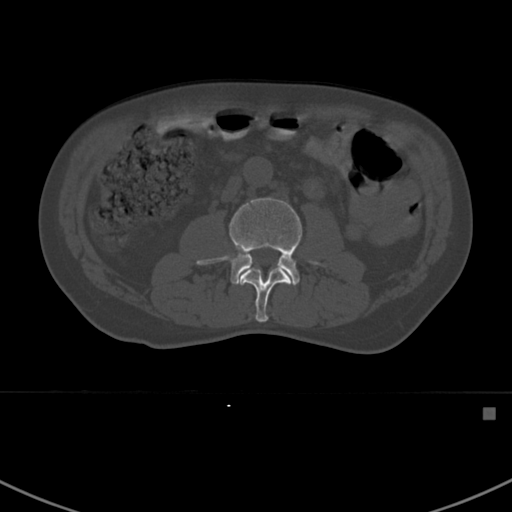
CT including the spine, one axial slice; position 273 of 412 along the scan axis; reconstruction kernel Br40s; 120 kVp; bone window (W 1800 / L 400 HU); 1.5 mm slice thickness; 512 × 512 image matrix, field of view 358 × 358 mm. Patient: male, 59 years. From the clinical record (not read from this slice): primary cancer: prostate.
Structures marked on this image (semi-automatic segmentation, software-assisted and operator-edited):
- L2 vertebra: box from (x=240, y=267) to (x=292, y=322) px
- L3 vertebra: (x=196, y=197)–(x=327, y=285)